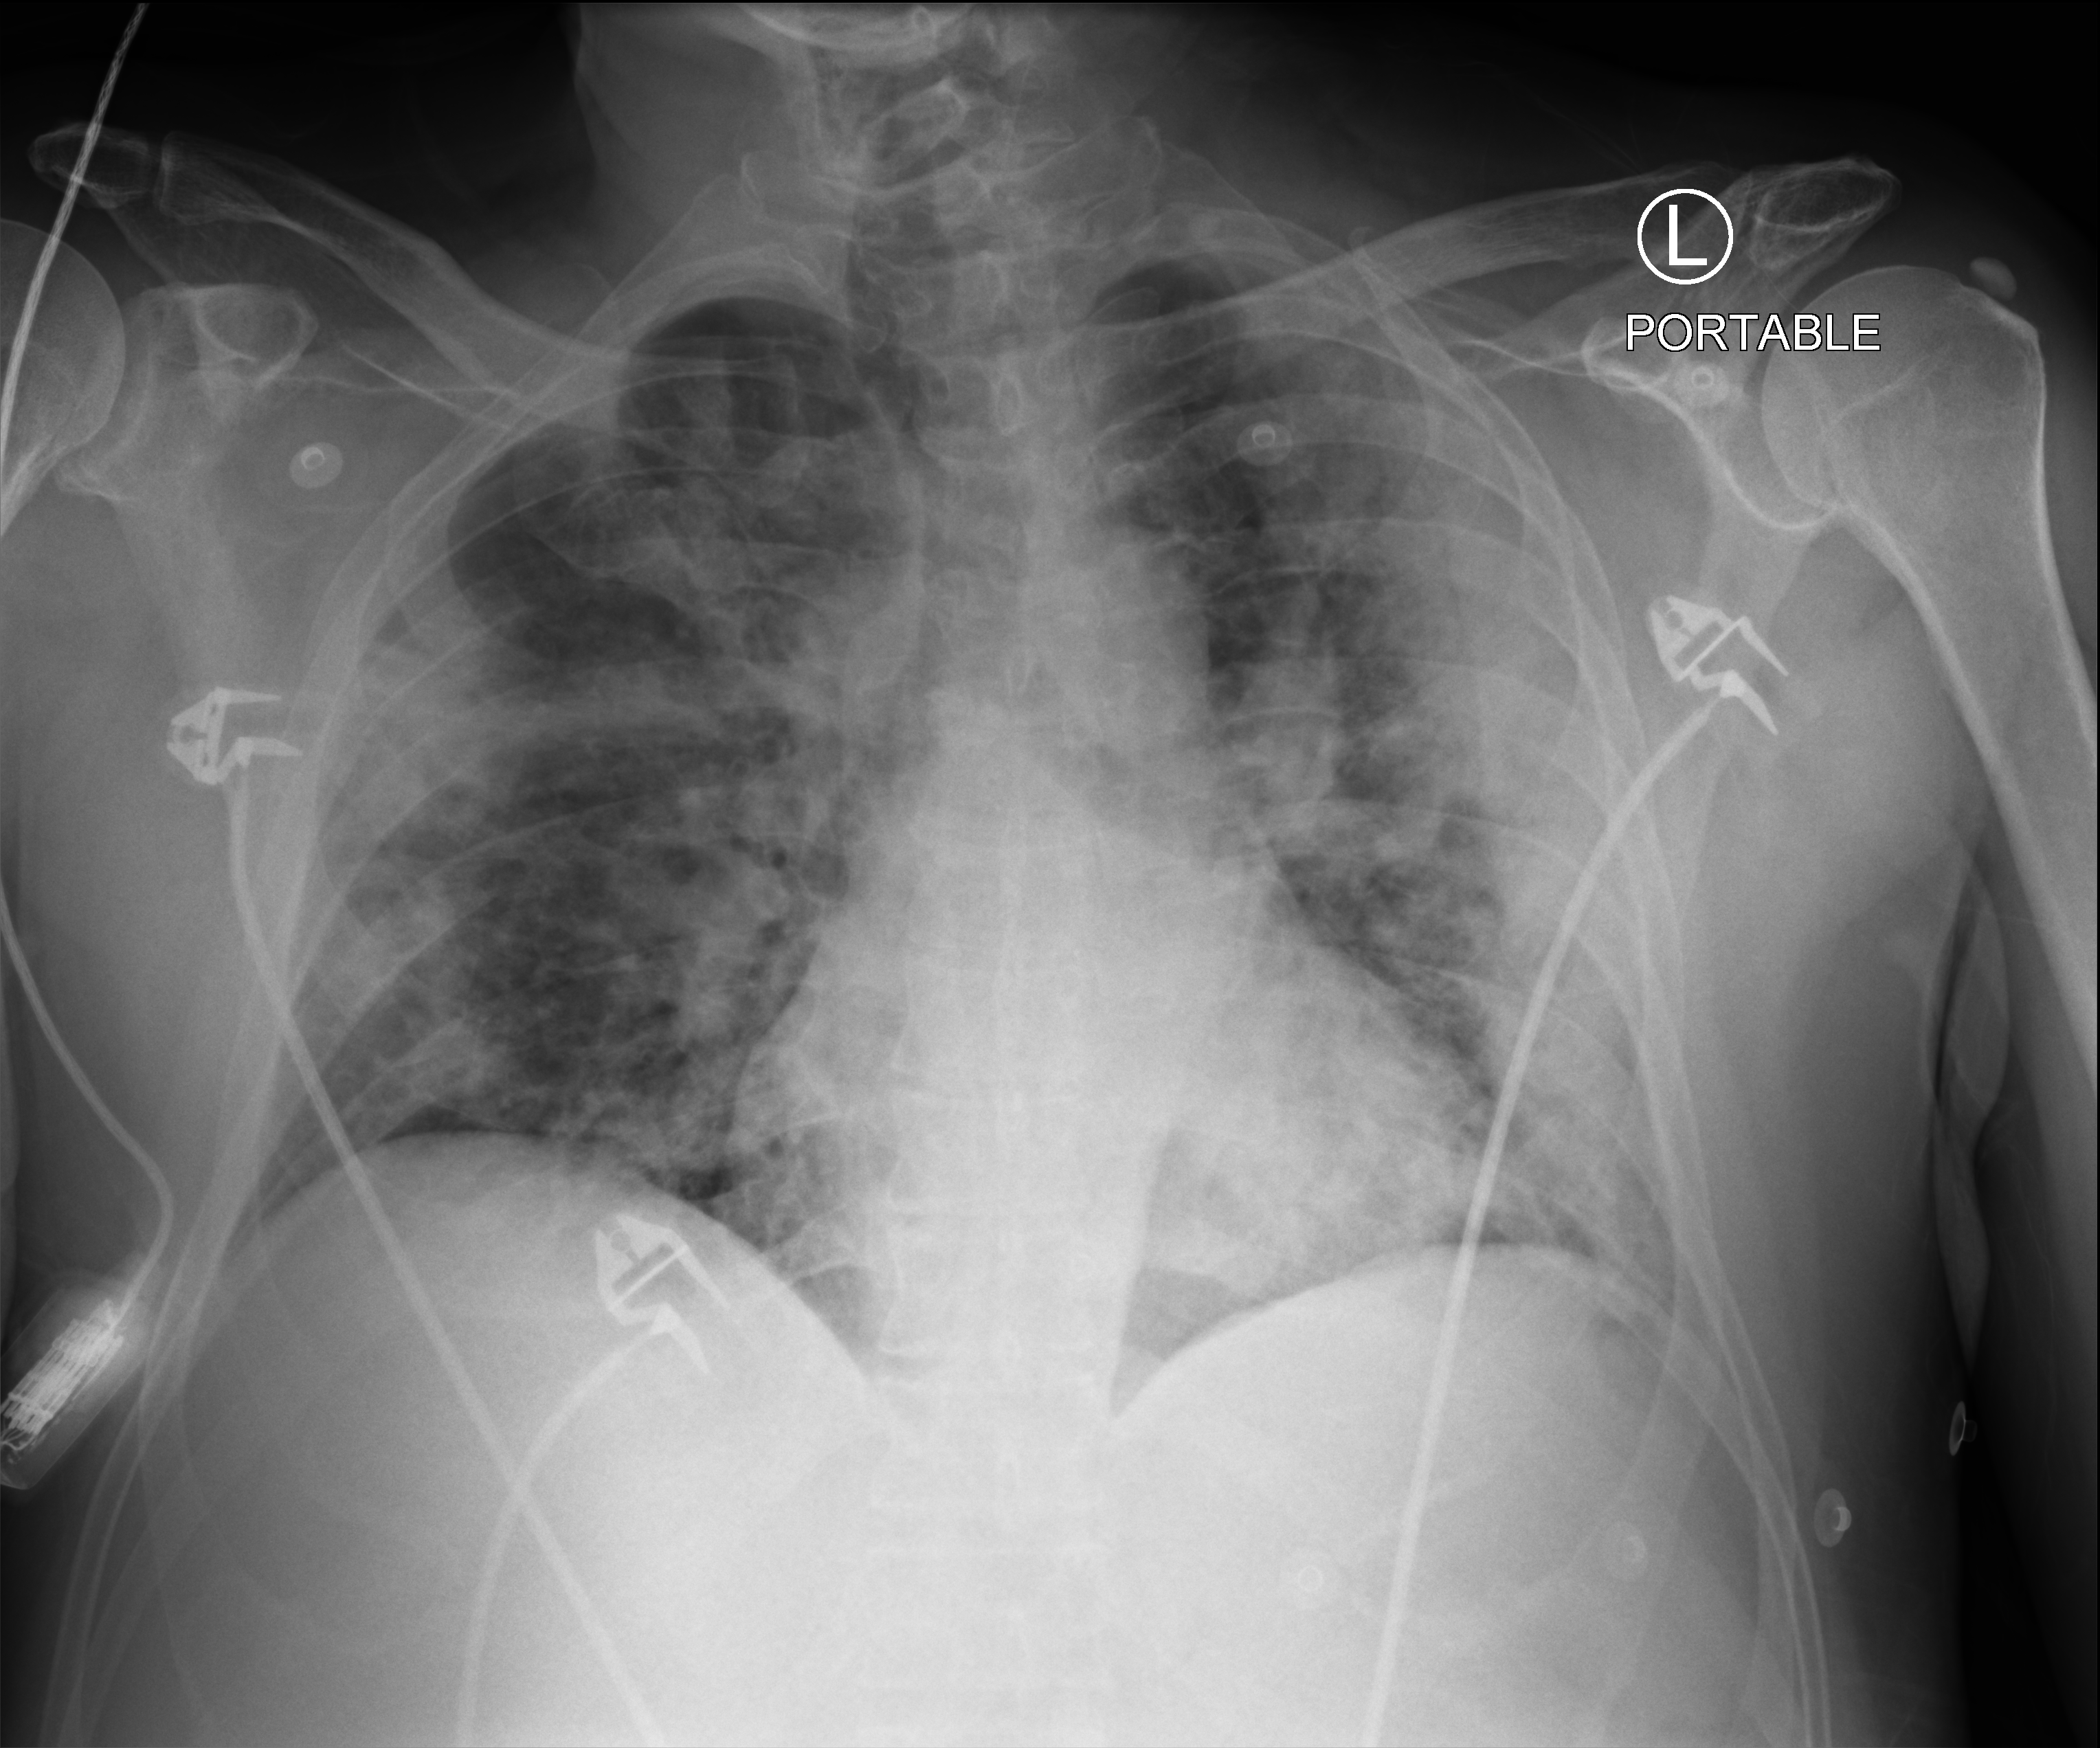
Chest X-ray (portable), anteroposterior (AP) projection. Male patient hospitalised with COVID-19, age 18–59 years.
Admission-level facts for this patient (not findings on this image; timing relative to this image not recorded):
- mechanically ventilated during this hospital stay: yes